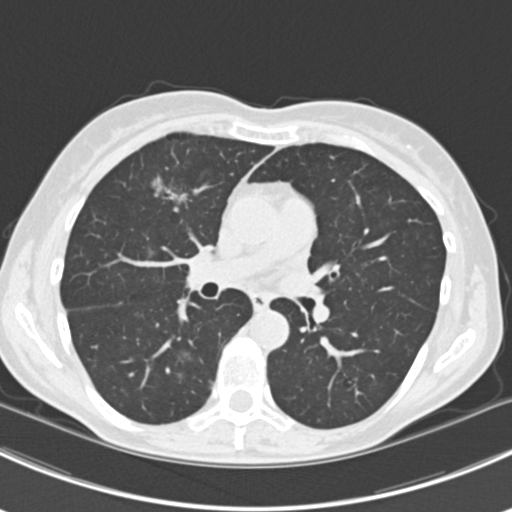
Axial slice from a low-dose chest CT screening exam, baseline screening round, lung window (W 1500 / L -600 HU), 2 mm slice thickness, slice 83 of 224 in the series. Female, age 63 years at enrolment. Current smoker at enrolment.
Lesion marked by an expert reader, bounding box [x1, y1, x2, y2] px = [144, 166, 202, 222]. The screening reader recorded 10 non-calcified nodules or masses ≥4 mm on this exam (right lower lobe, right lower lobe, left lower lobe, left lower lobe, right middle lobe, right lower lobe, left lower lobe, left upper lobe, right upper lobe, left upper lobe); which of them this box marks is not recorded. Lung cancer was diagnosed 751 days after this screen: bronchiolo-alveolar adenocarcinoma, NOS, right upper lobe, right middle lobe, right lower lobe, left upper lobe, left lower lobe, moderately differentiated (G2), stage IV (AJCC 6th edition).